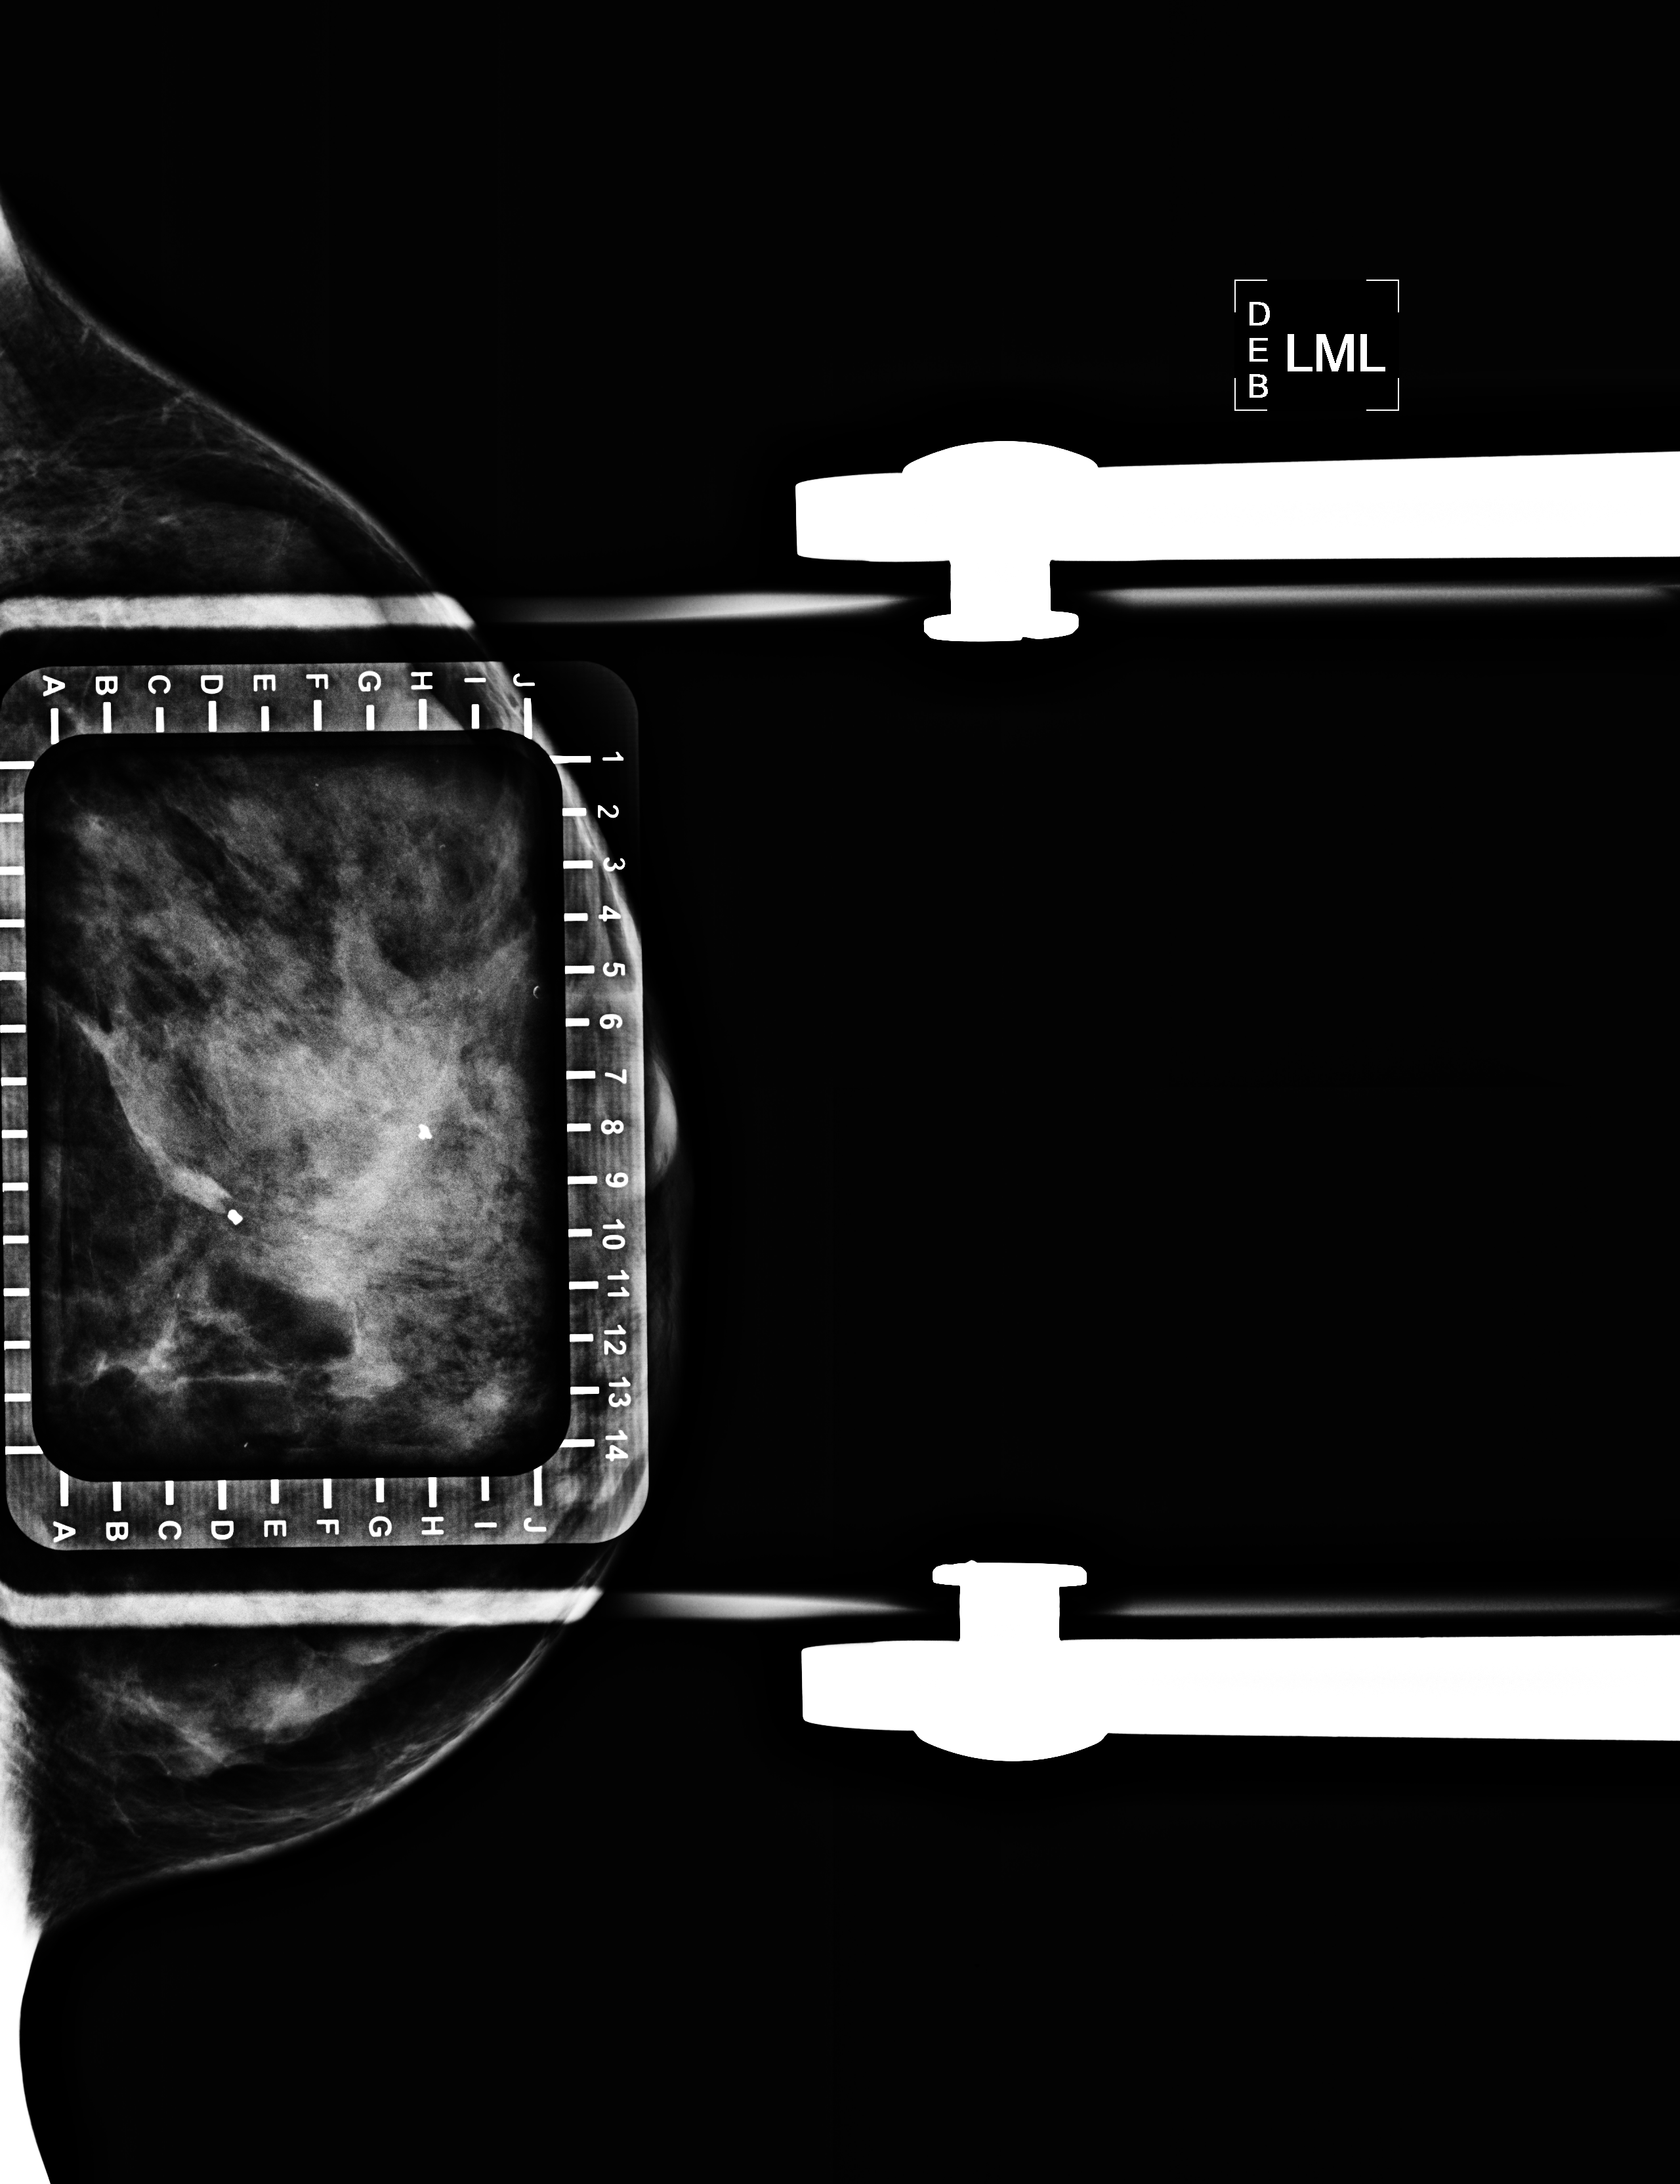
Needle-localisation mammographic view, left breast, ML view.
Pathology recorded for this patient (not read from this image): pathology diagnosis: ducta CA in situ (left breast); receptor status (as recorded): ER neg, PR neg, HER2 pos.